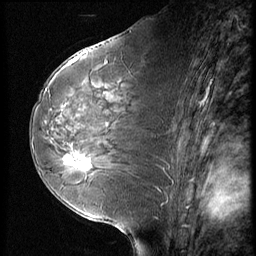
Breast MRI (dynamic contrast-enhanced), one sagittal slice; slice 33 of 56 in the series (ordered by position); dynamic contrast-enhanced series, image 2 of 3 at this slice position (ordered by acquisition); 1.5 T; TE 4.2 ms, TR 9 ms; 2.5 mm slice thickness; 256 × 256 image matrix. Female patient, age 58 years. From the clinical record (not read from this slice): setting: breast cancer imaged before/during neoadjuvant chemotherapy; receptor status: HR-positive, HER2-negative.
Outlined on this slice (semi-automatic segmentation, software-assisted and operator-edited):
- analysis volume of interest (the breast-tissue region the enhancement analysis was run in; not a lesion): bounding box (x1, y1, x2, y2) in pixels: (56, 146, 99, 182)
- tumour enhancement mask (voxels above the 140 % enhancement threshold inside the analysis volume of interest): (63, 152, 90, 169)